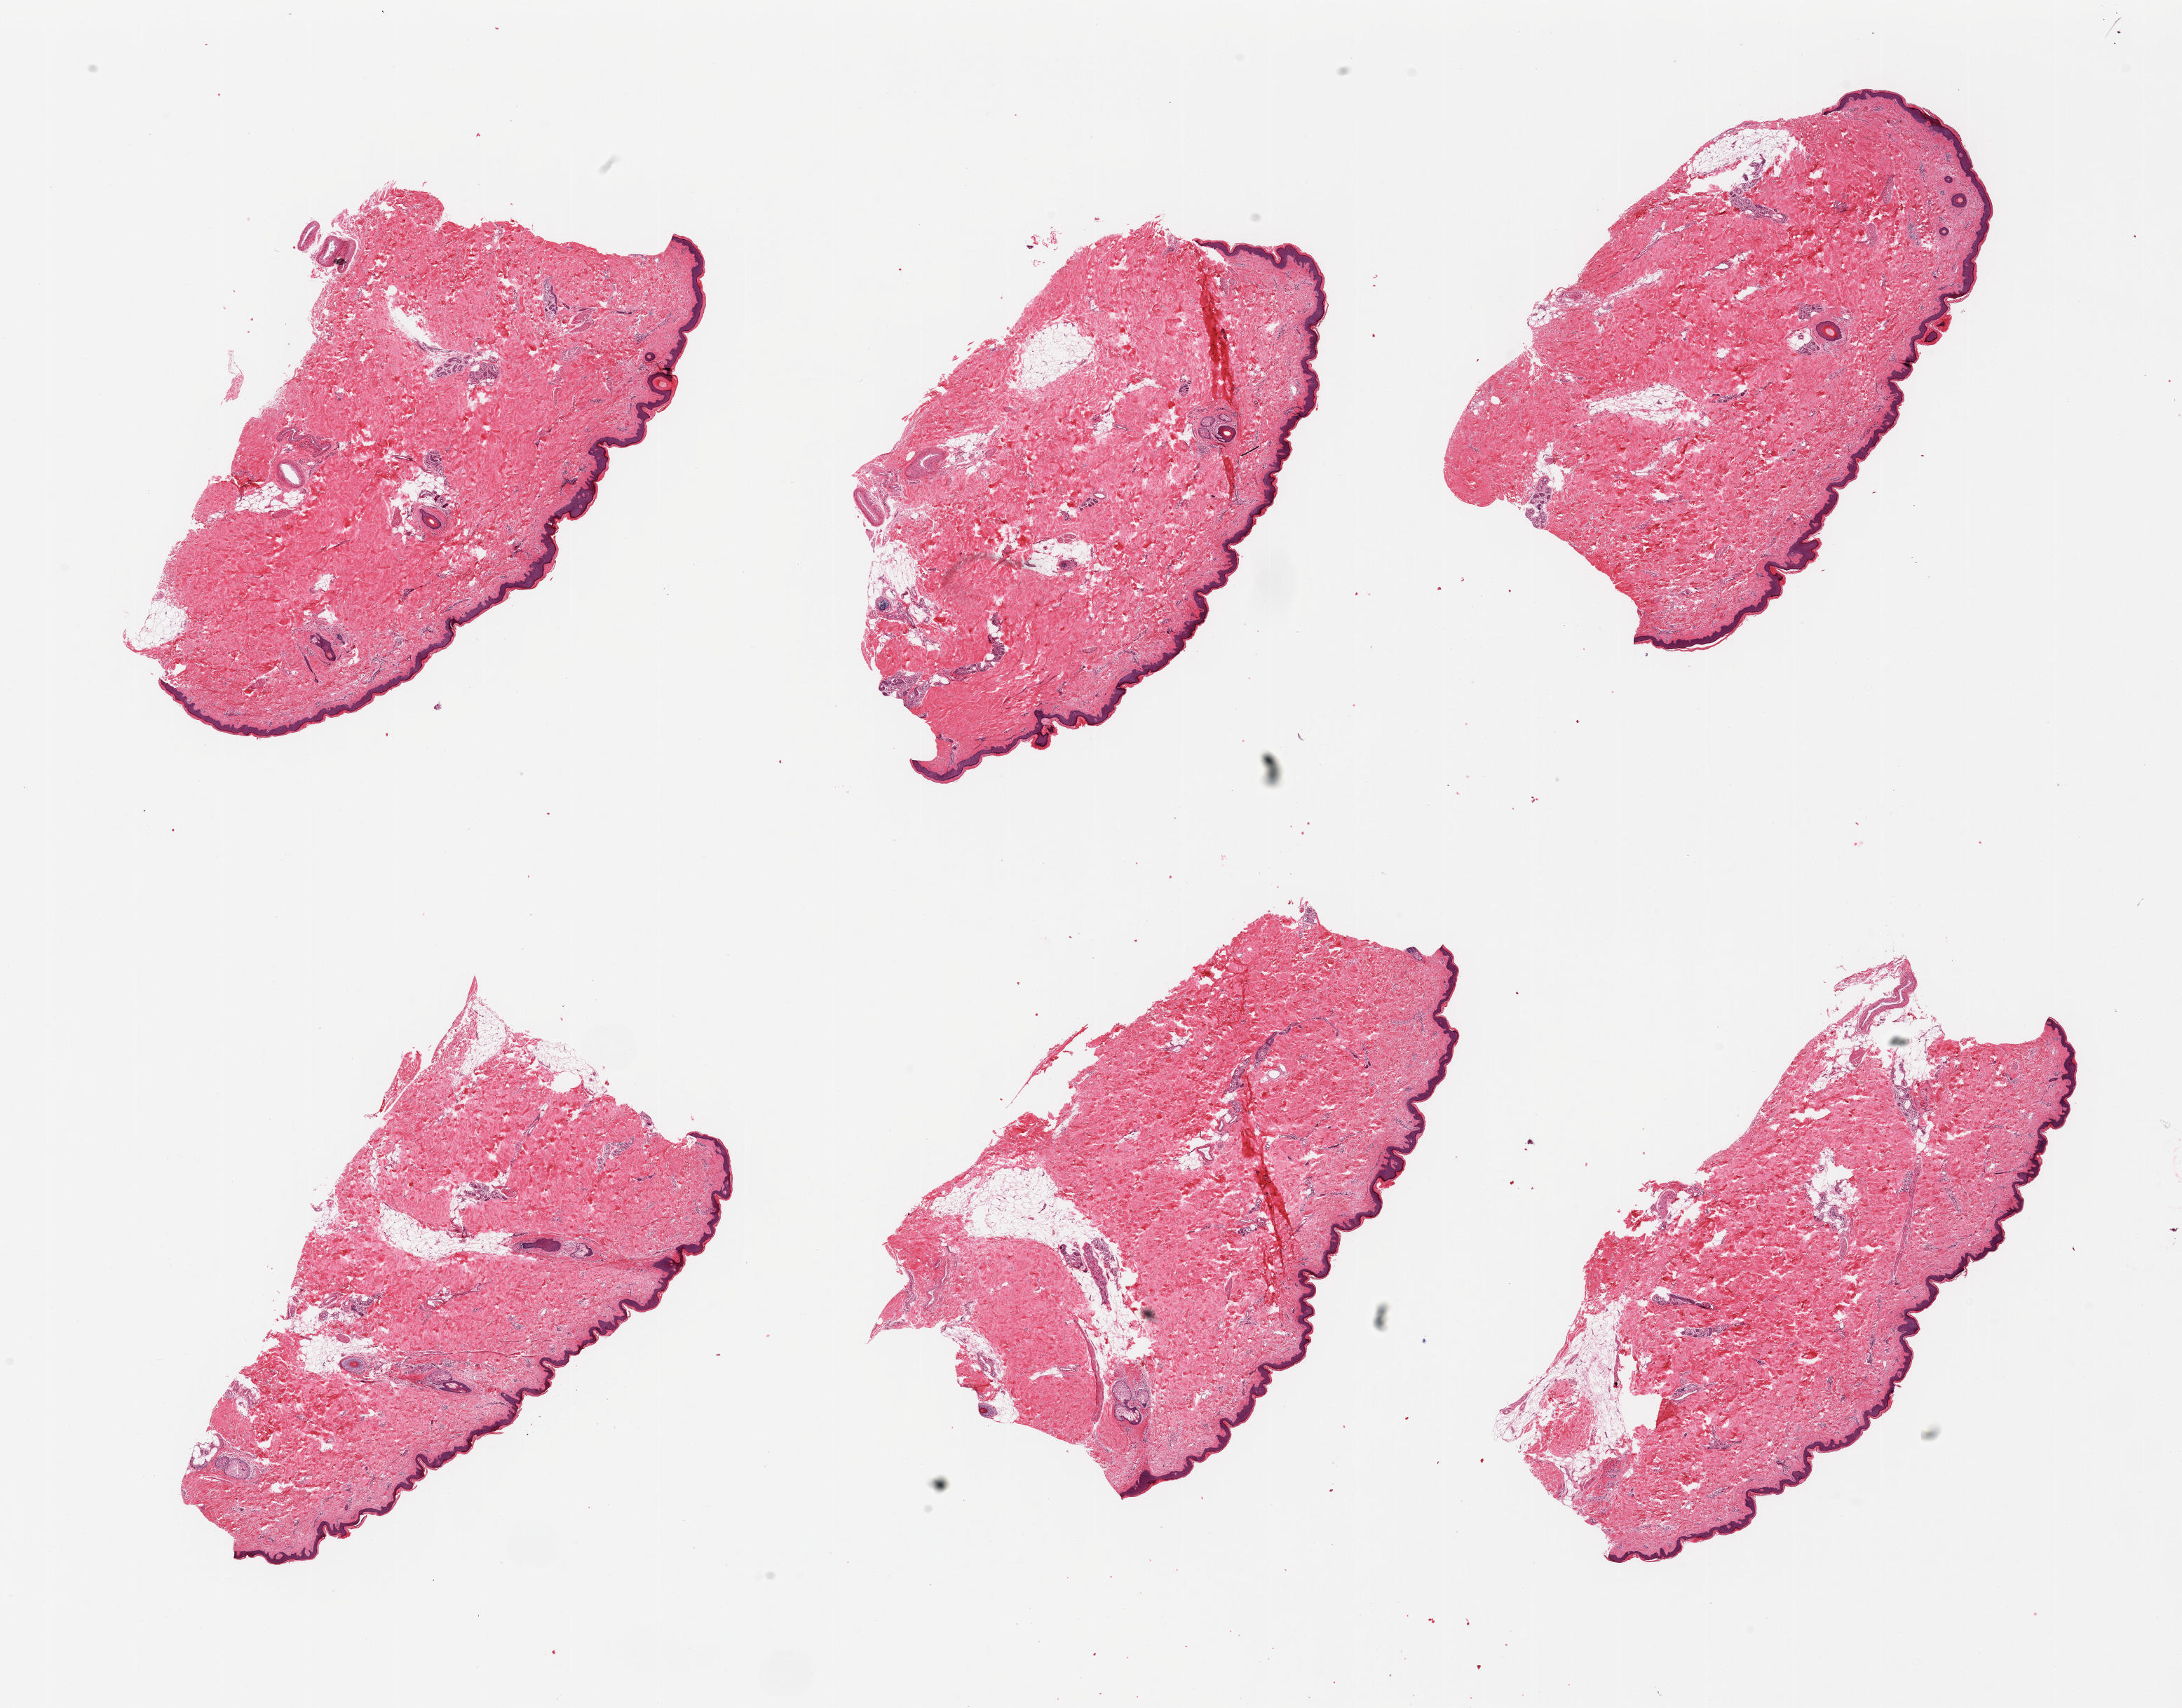
Whole-slide image, H&E stain — whole scanned area (about 24.6 x 19.3 mm) shown as a low-resolution overview. PAXgene-fixed, paraffin-embedded tissue. Section of skin of lower leg (target tissue). Donor tissue sample. Donor: male.
• pathologist's review note for this sample: 6 pieces, trace dermal fat; squamous epithelium is ~50-60 microns